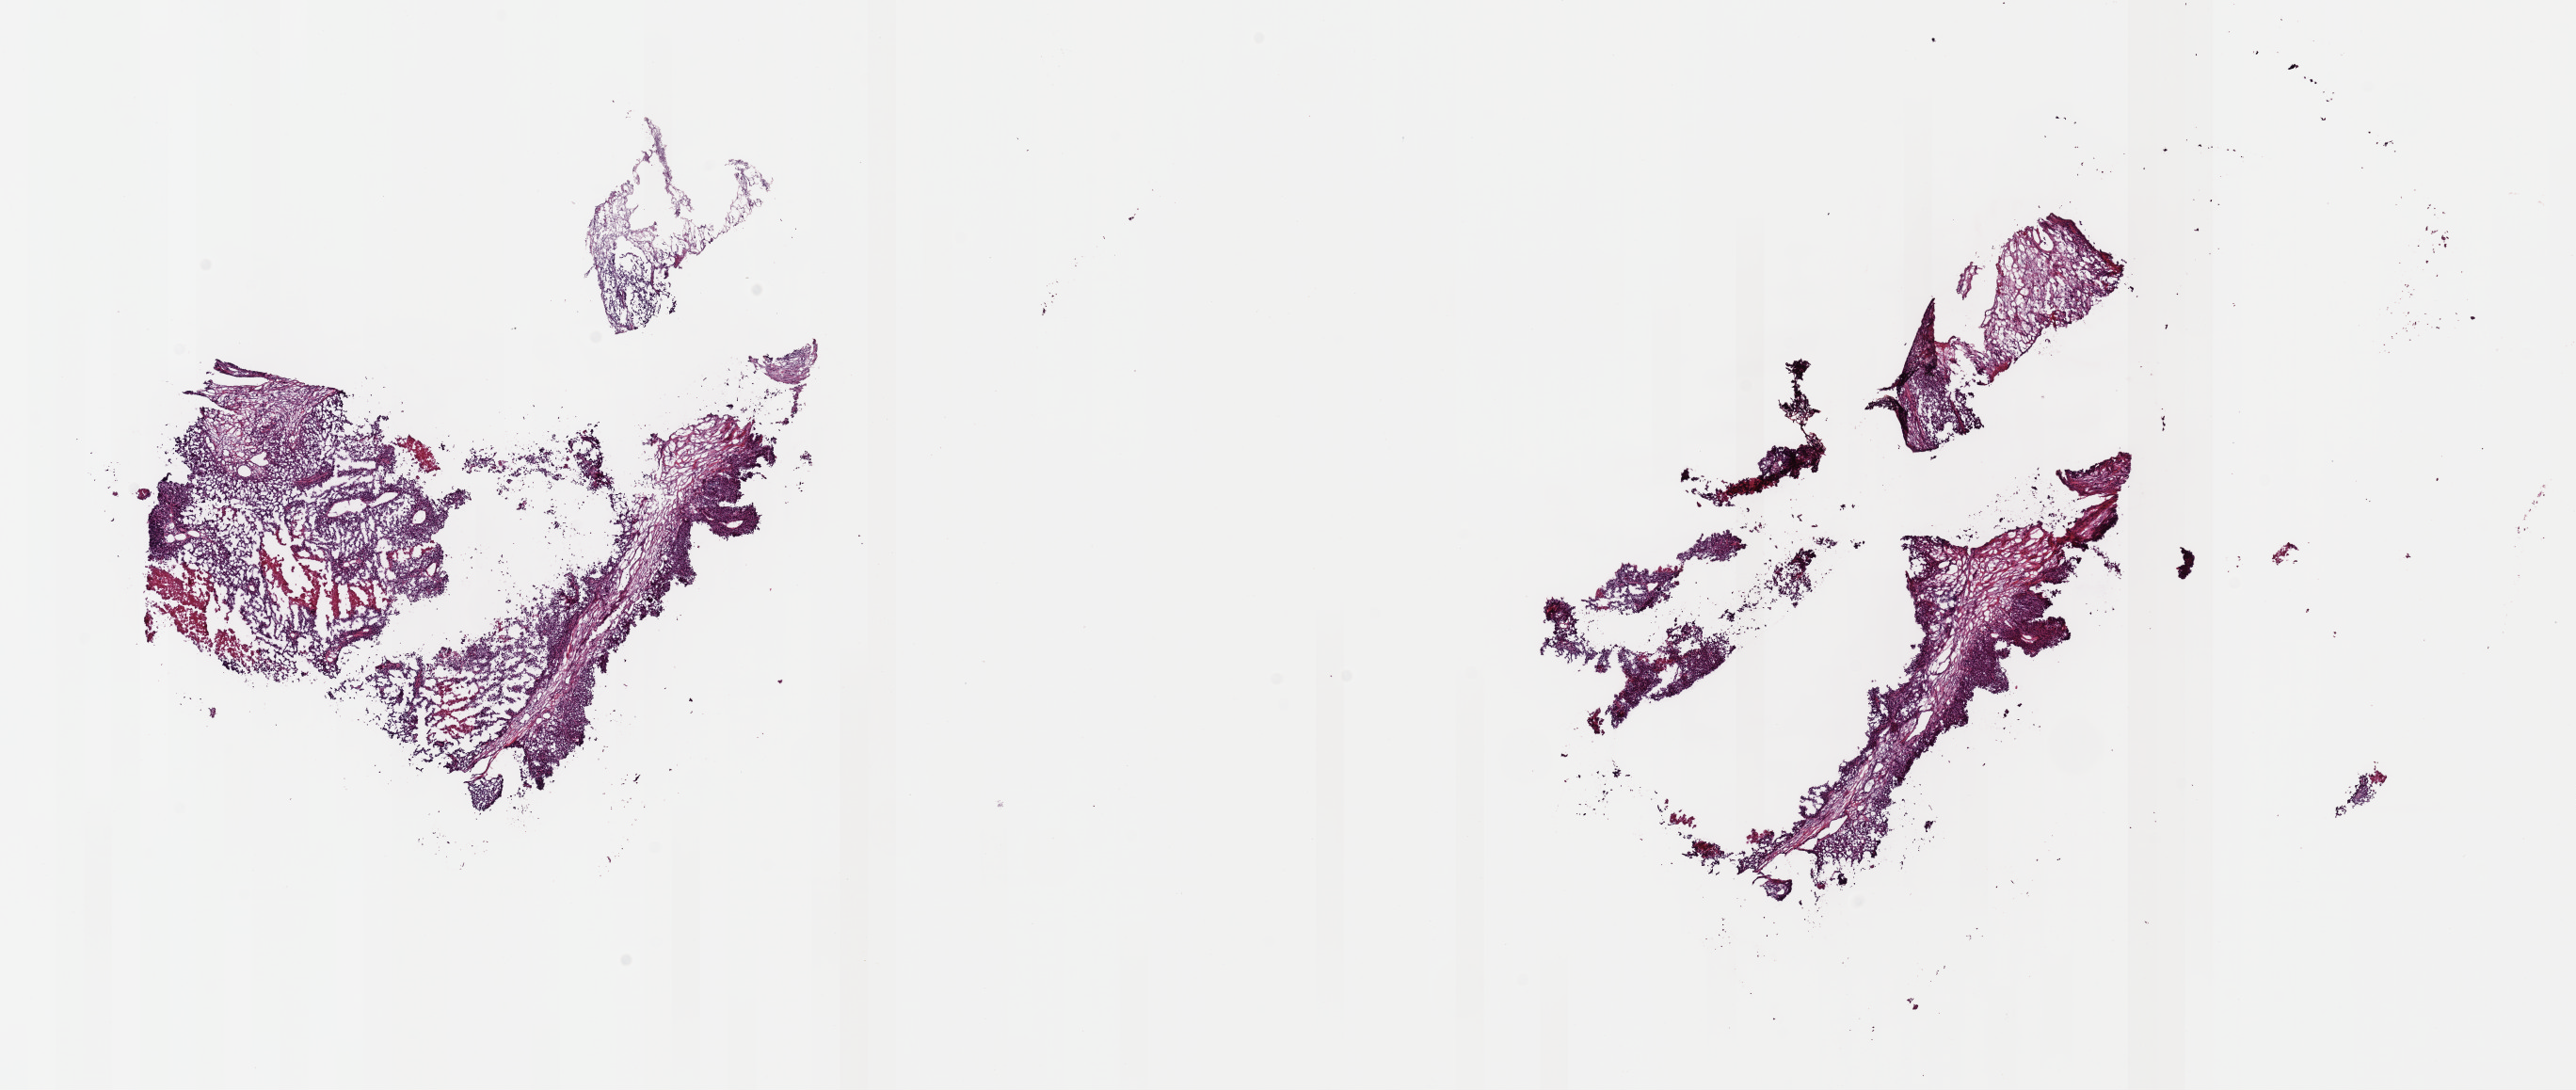
H&E-stained whole-slide image — a low-resolution overview of the entire scanned area, about 21.6 x 9.1 mm (from a 40x scan); frozen section from the top of the tissue portion; metastatic tumour sample, sampled site: lymph nodes of inguinal region or leg. Female, age 57 years at initial diagnosis. Composition of this section per pathologist review: tumour cells 65%, tumour nuclei 80%, normal cells 20%, stromal cells 0%, necrosis 15%. Inflammatory infiltration, as recorded: lymphocyte infiltration 1%, monocyte infiltration 8%, neutrophil infiltration 0%.
This section: metastatic tumour tissue. Patient diagnosis: Malignant melanoma, NOS.